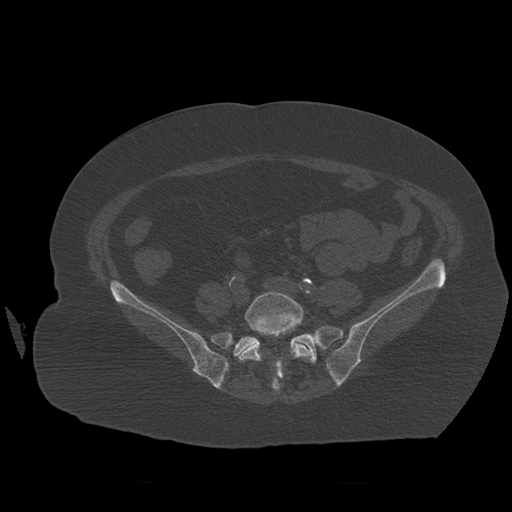
CT including the spine, one axial slice. Position 175 of 399 along the scan axis. Bone window (W 1800 / L 400 HU). 512 × 512 image matrix. Patient age 81 years. Case-level facts recorded for this patient, not image findings: primary cancer: renal.
Annotated regions visible in this slice (semi-automatic segmentation, software-assisted and operator-edited):
- L5 vertebra: bounding box (x1, y1, x2, y2) in pixels: (239, 292, 312, 362)